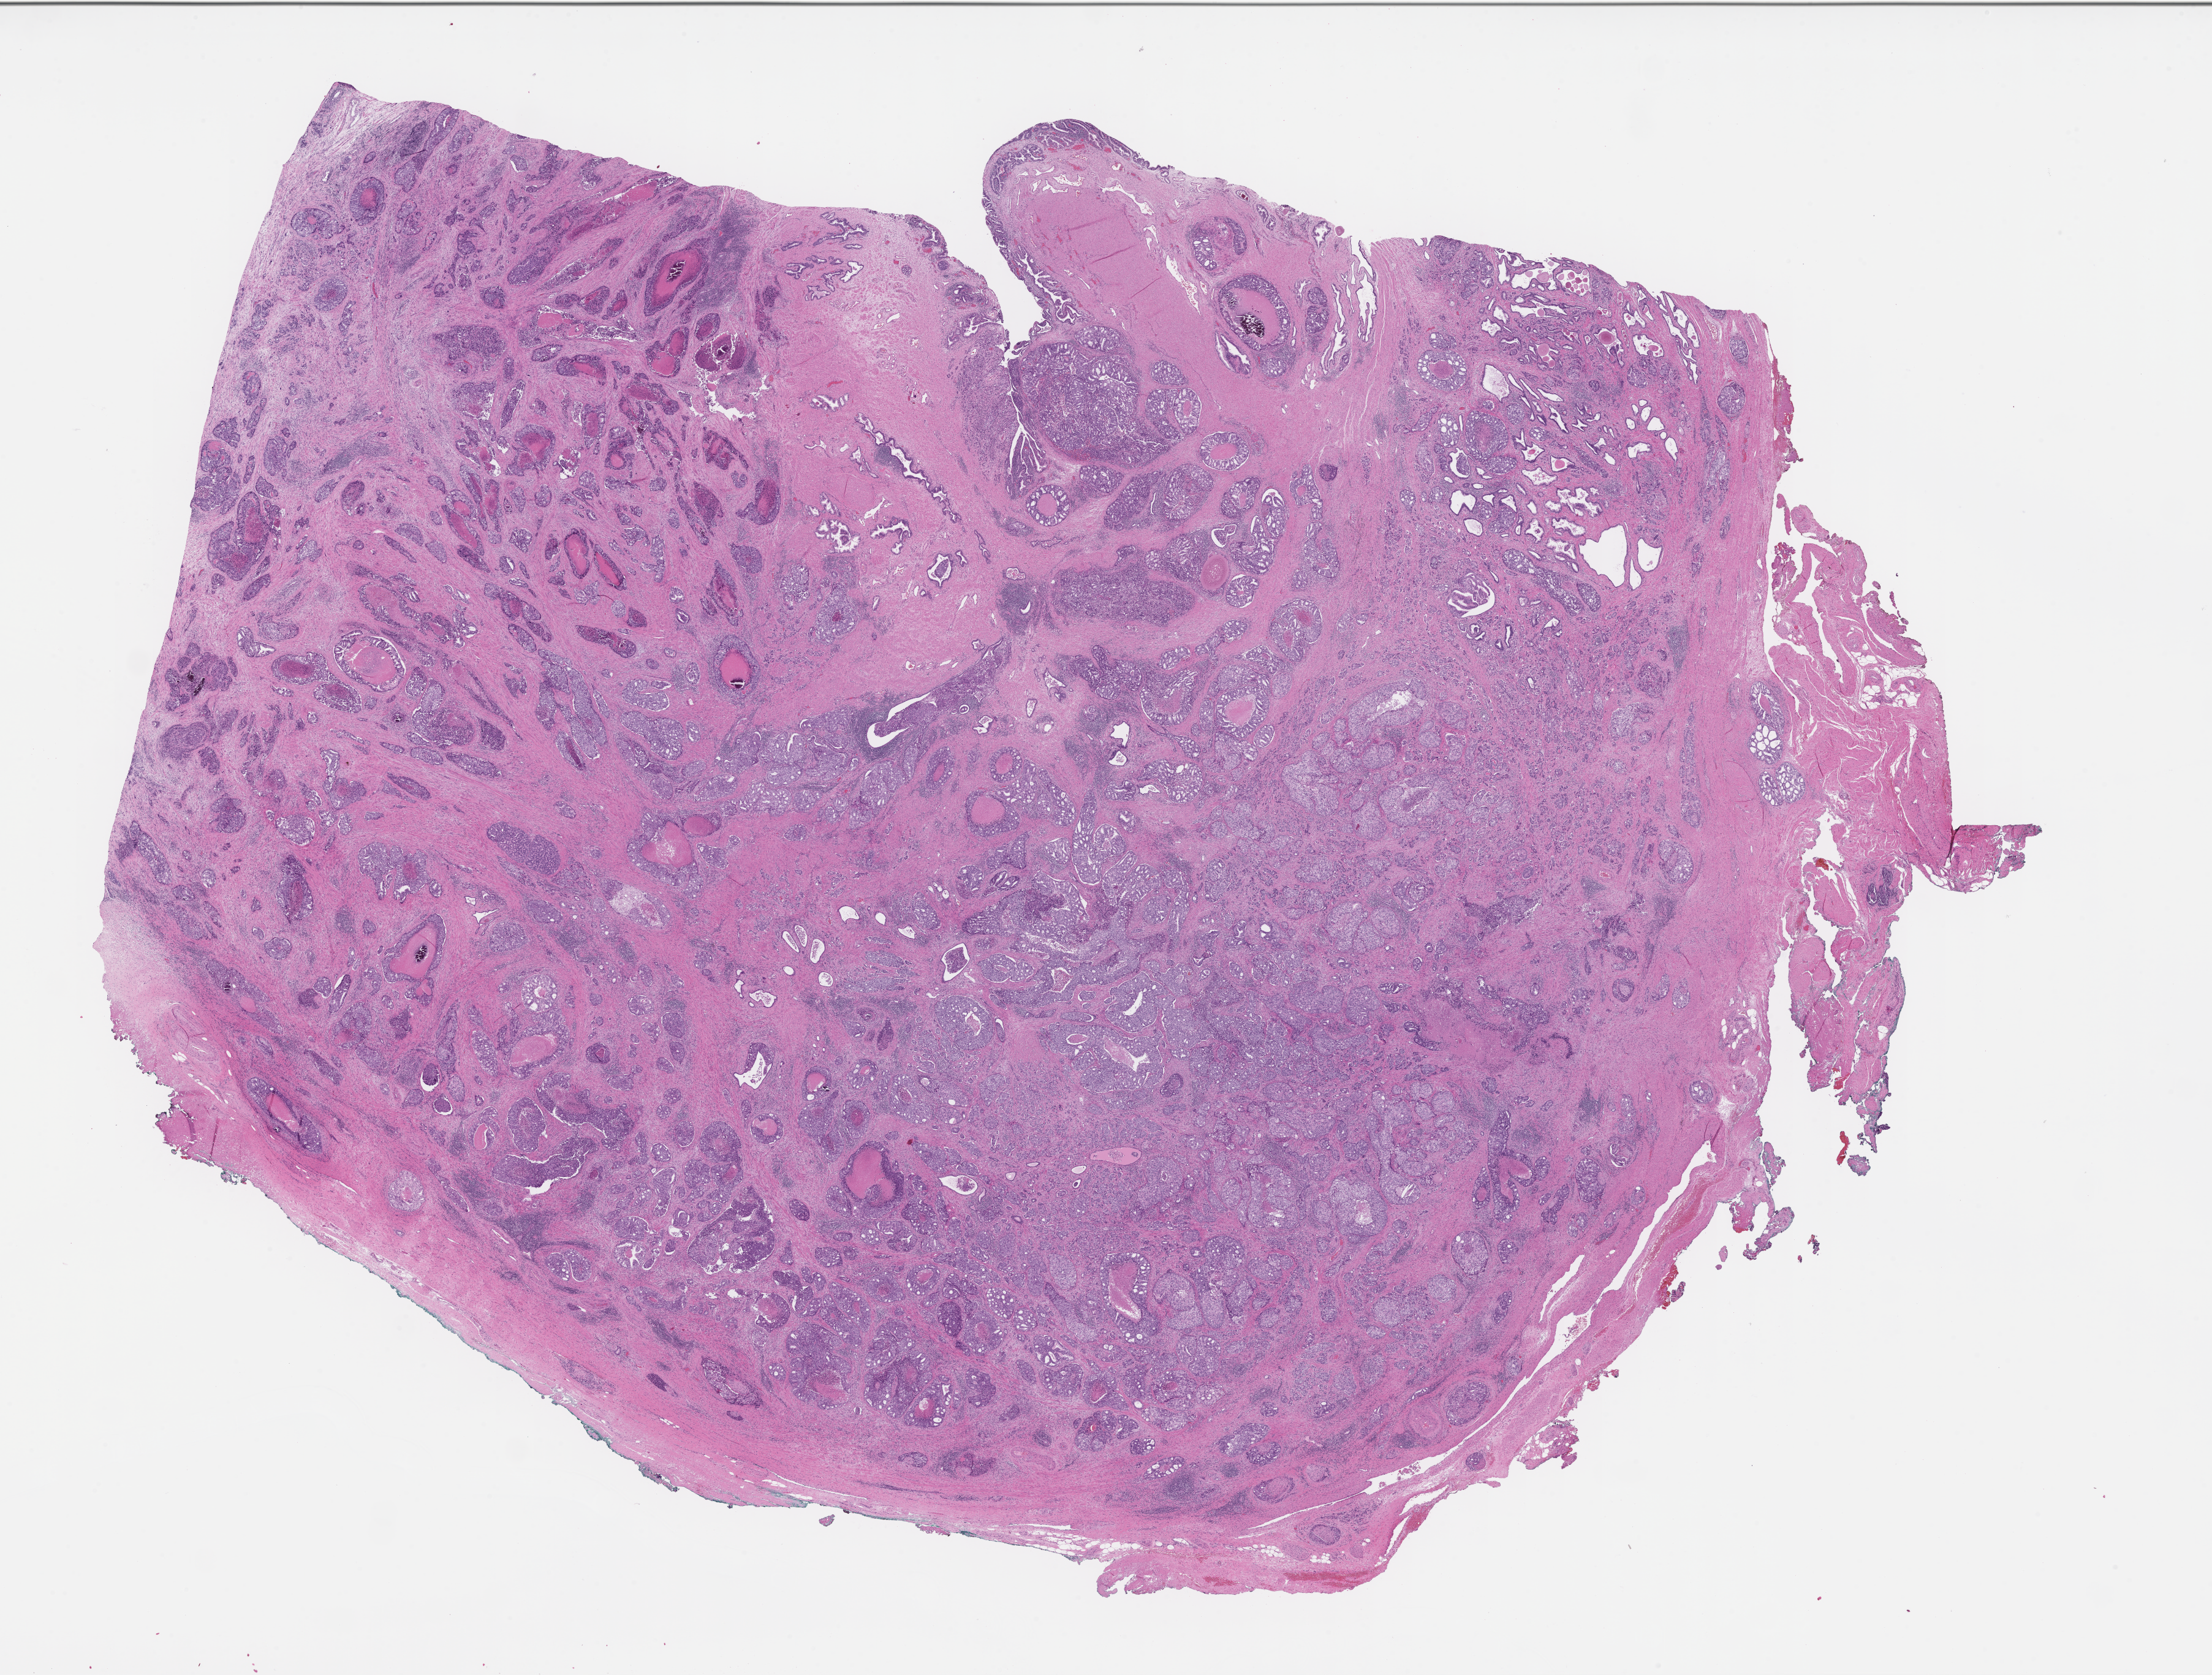
H&E whole-slide image, shown as a low-resolution overview of the whole scanned area (about 29.1 x 22.1 mm). Formalin-fixed paraffin-embedded section. Tissue site: prostate. Specimen time point: archival tissue. Male patient.
This section: primary tumour tissue. Diagnosis: Prostate Carcinoma.